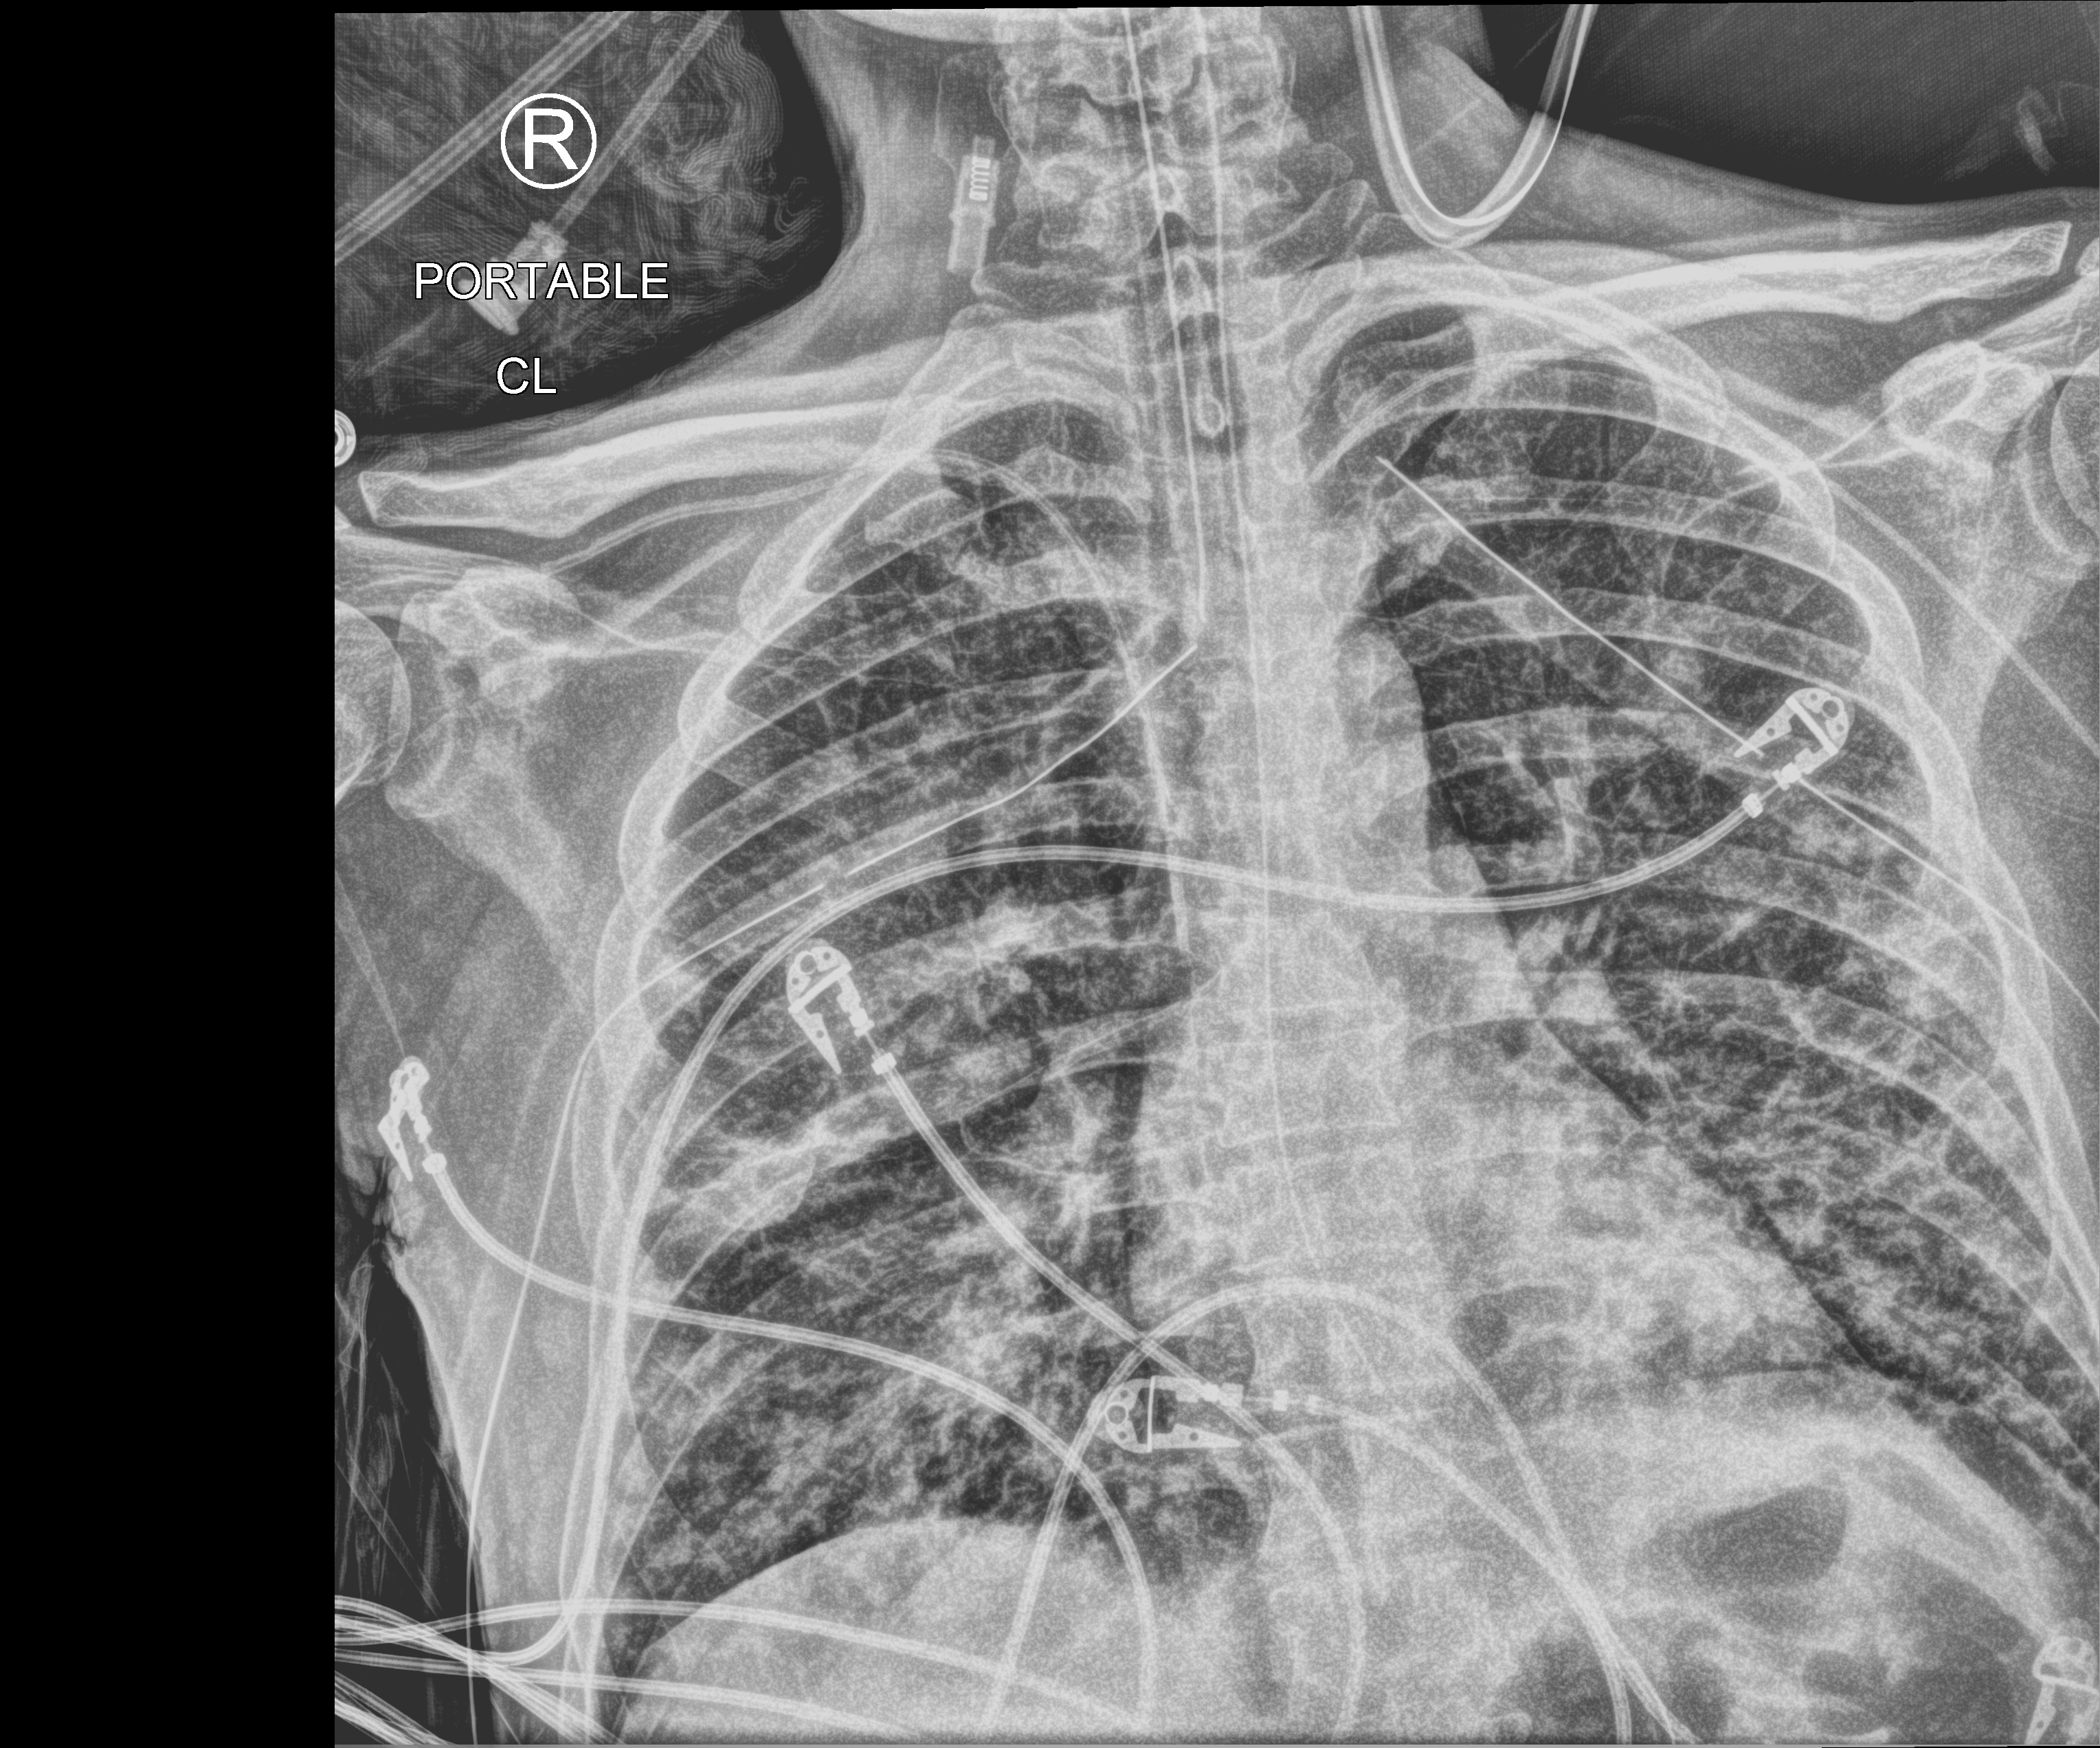
Bedside chest radiograph (computed radiography), anteroposterior (AP) projection. Patient hospitalised with COVID-19; male, aged 18–59 years.
Hospital-stay facts (about this admission, not read from this image; timing relative to this image not recorded): admitted to intensive care during this hospital stay: yes; diabetes (admission record): yes.